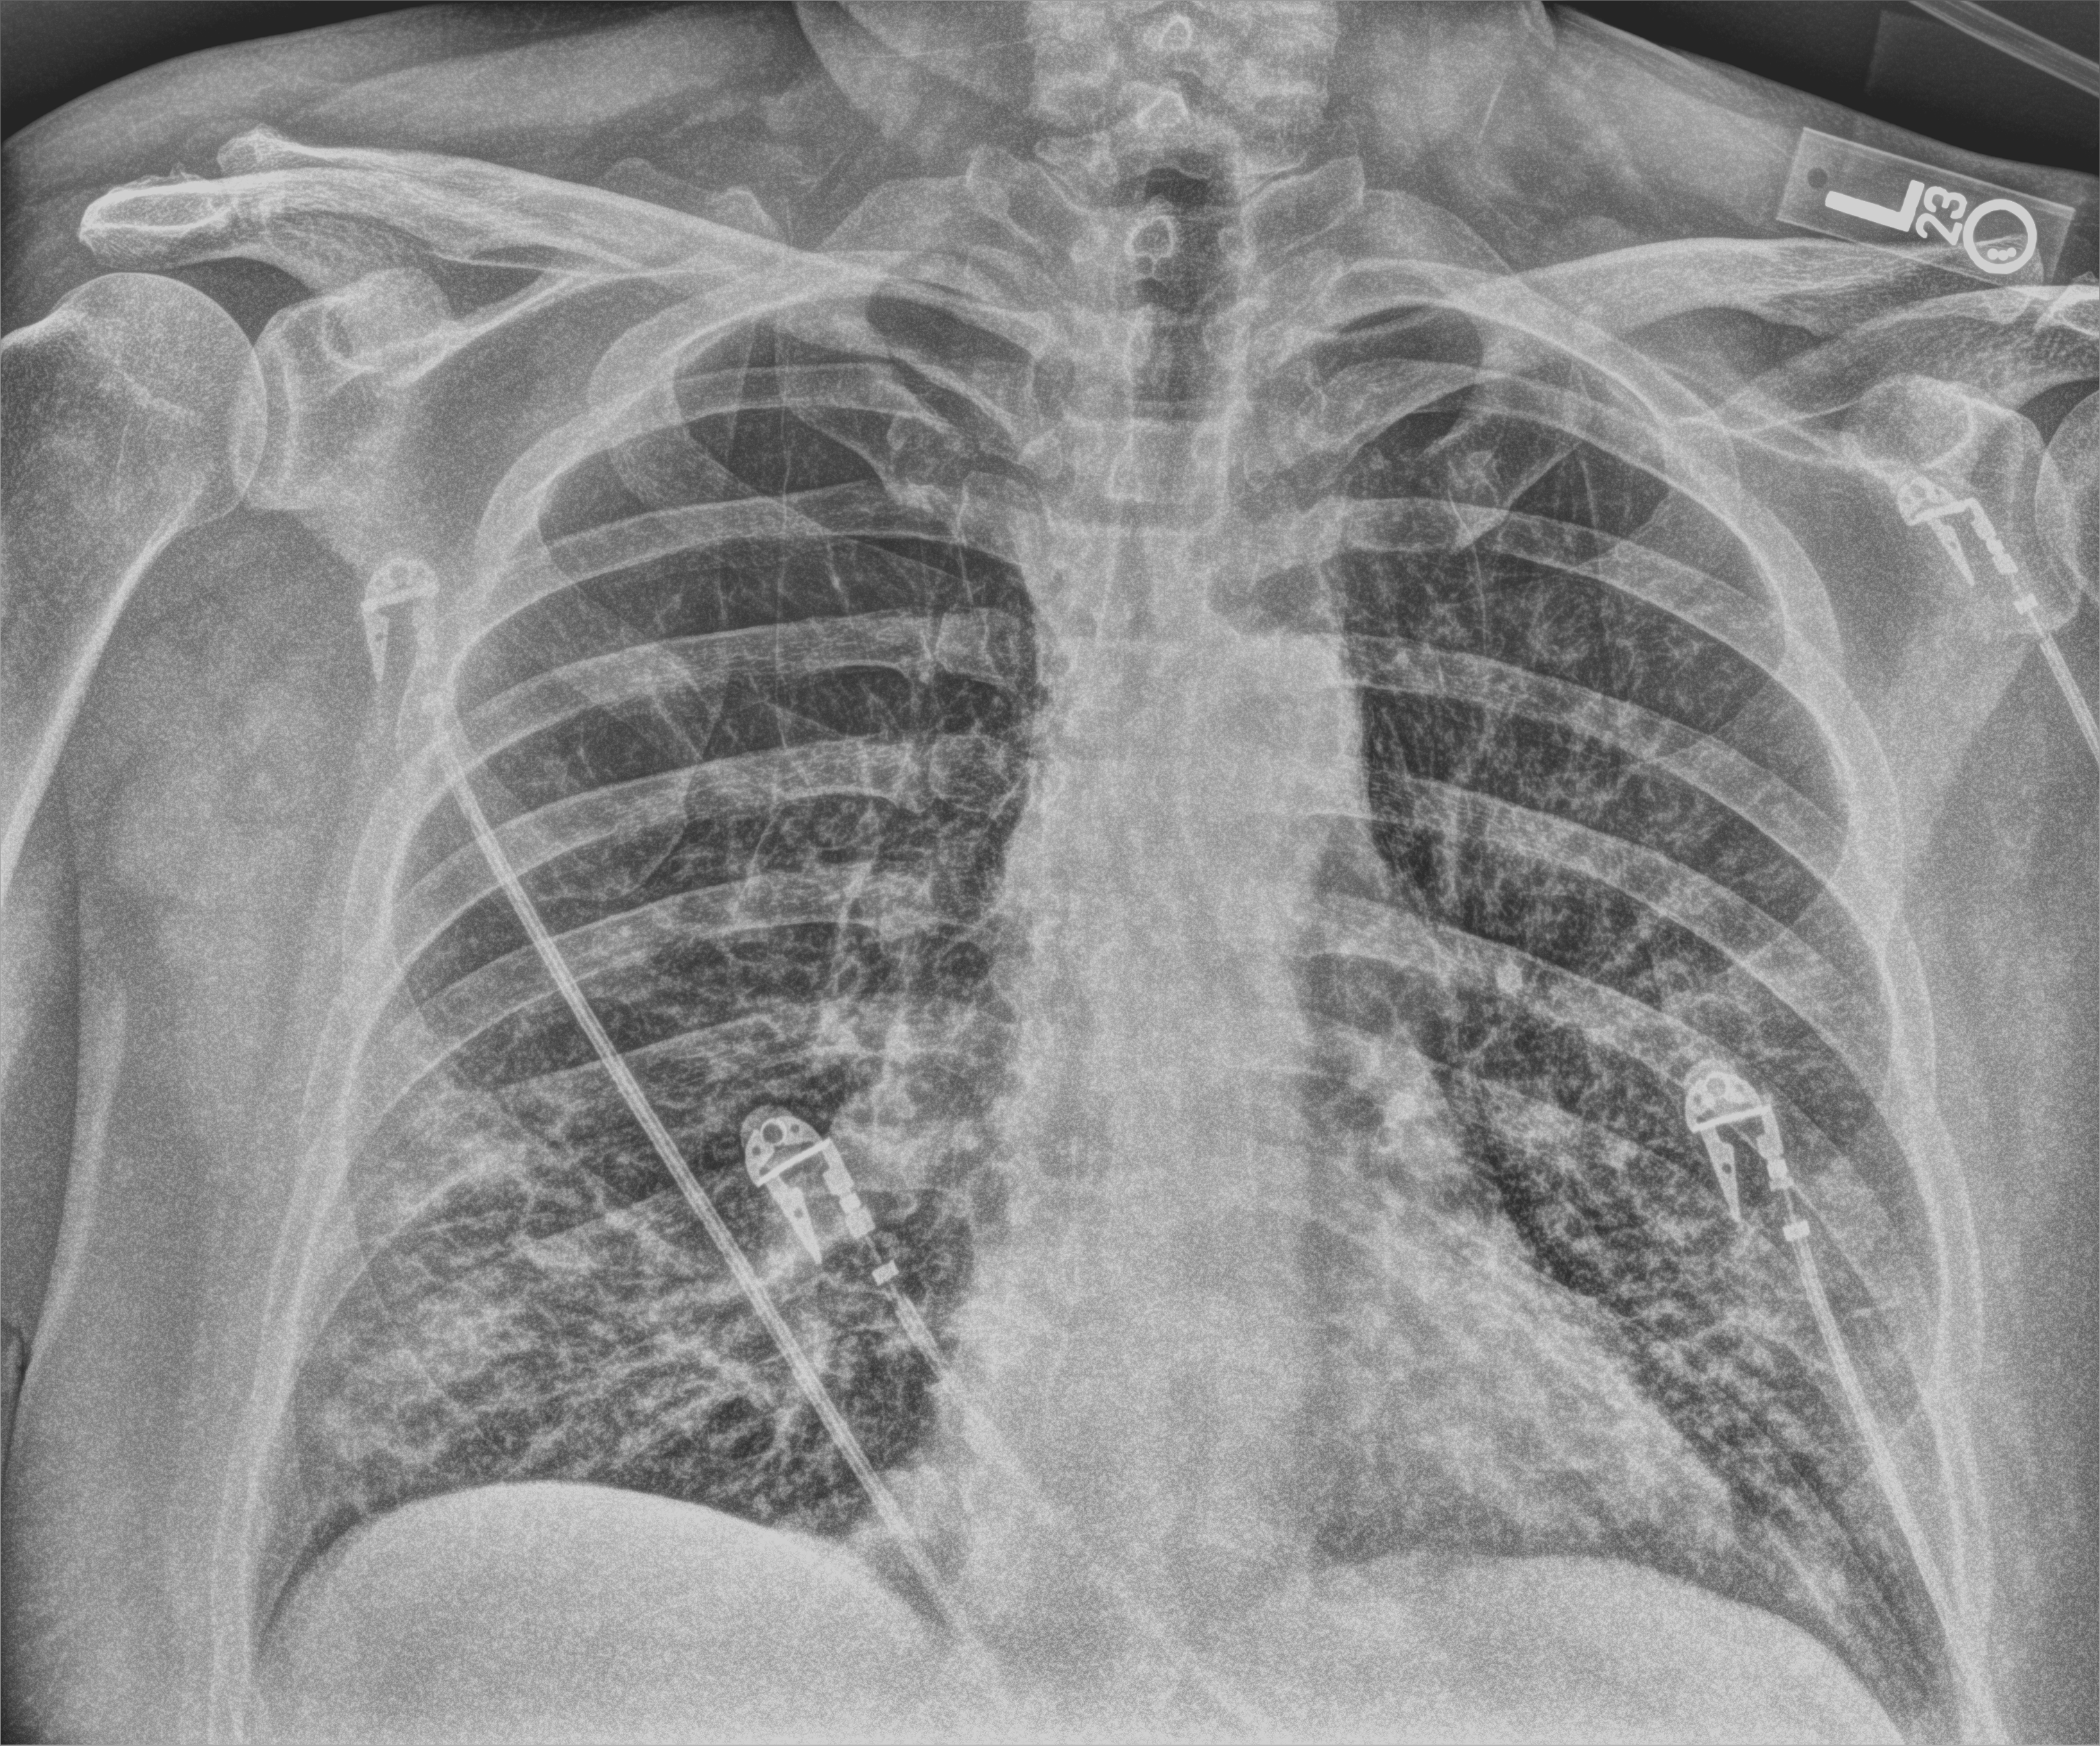
Chest X-ray (portable). Patient hospitalised with COVID-19, aged 18–59 years.
From the hospital-stay record, not from the radiograph (when in the stay this image was taken is not recorded): admitted to intensive care during this hospital stay: yes; mechanically ventilated during this hospital stay: yes.